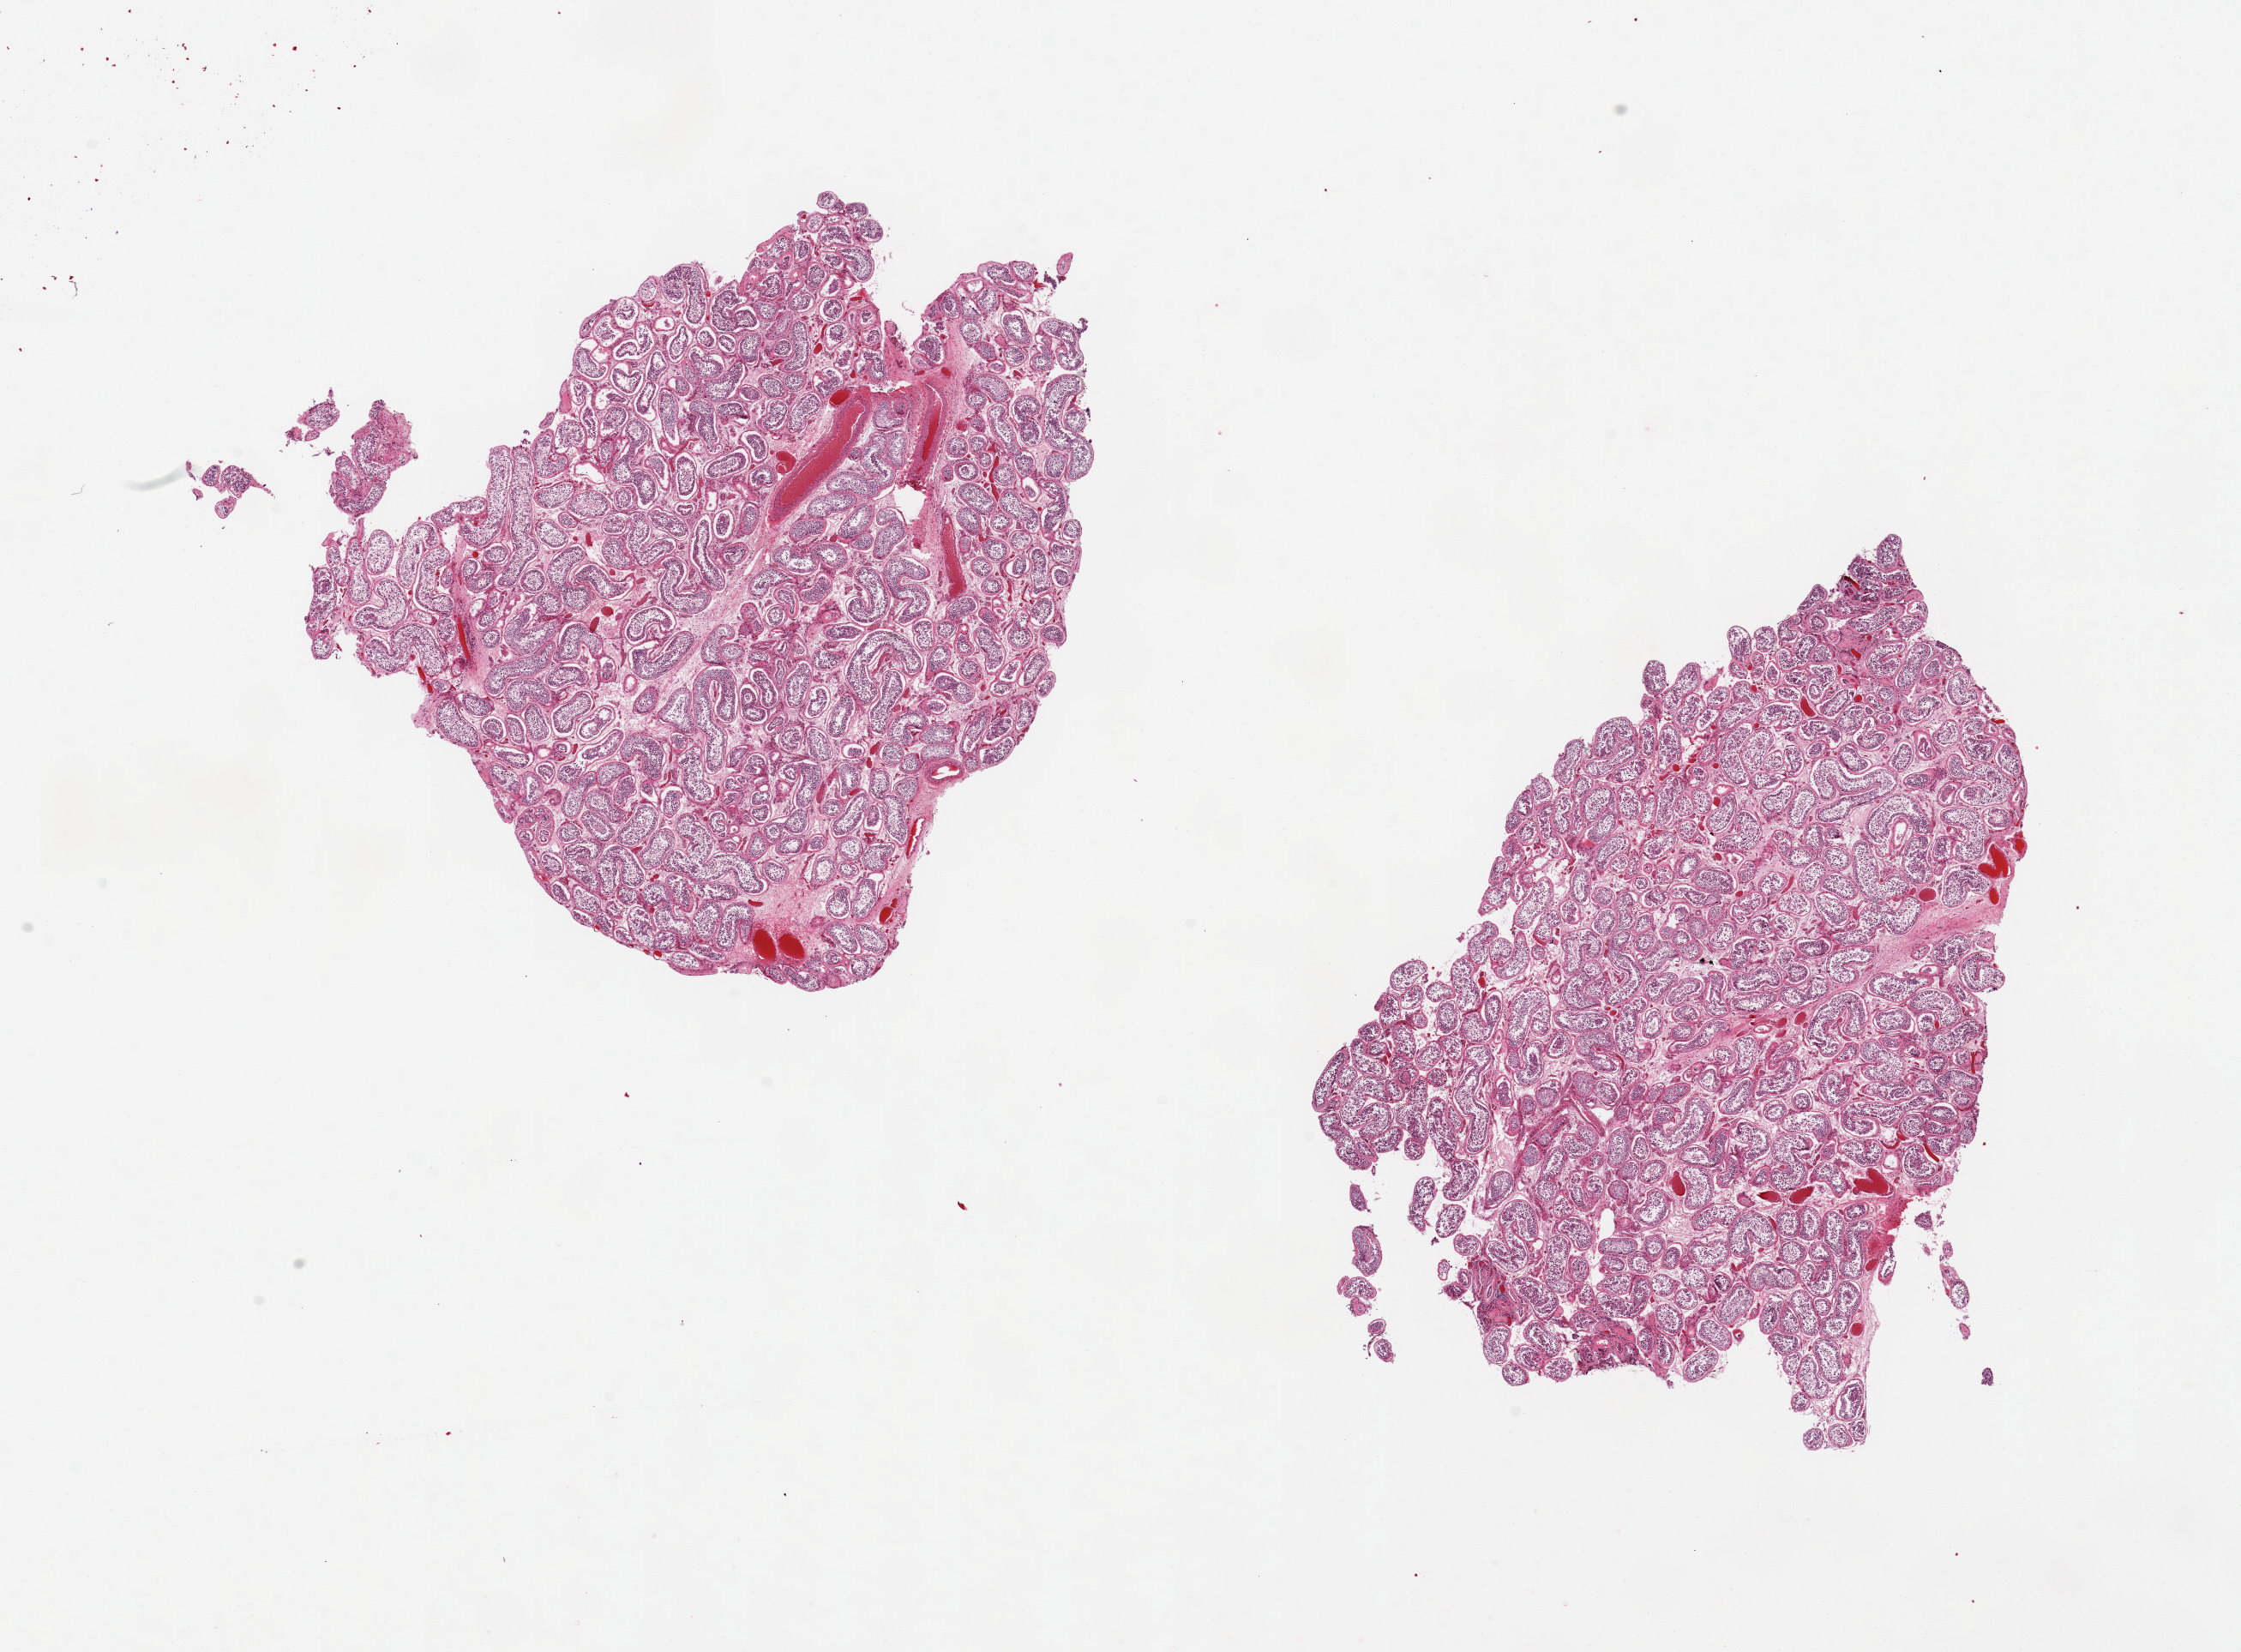
Whole-slide image, haematoxylin and eosin stain — low-resolution overview of the scanned area, about 20.7 x 15.2 mm (acquisition: 20x scan). PAXgene-fixed paraffin-embedded (PFPE) section. Section of testis (target tissue). Donor tissue sample. Donor sex: male.
• pathologist's review note for this sample: 2 pieces 8x5 & 7x6 mm;spermatogenesis